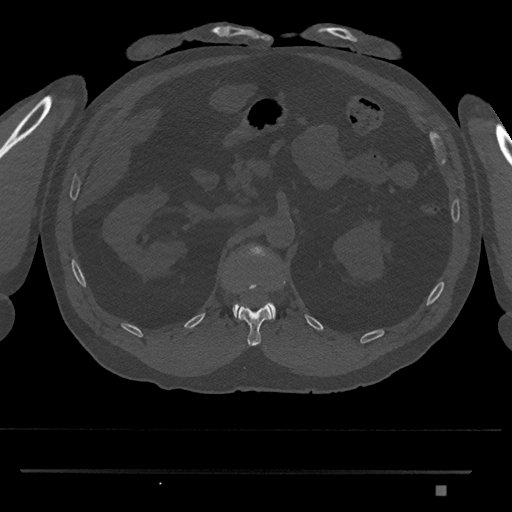
CT including the spine, one axial slice; position 862 of 1134 along the scan axis; bone window (W 1800 / L 400 HU); 0.5 mm slice thickness; 512 × 512 image matrix. Patient: male, 65 years. Case-level facts recorded for this patient, not image findings: primary cancer: prostate.
Structures marked on this image (semi-automatically segmented with operator editing):
- L1 vertebra: box from (x=232, y=244) to (x=276, y=320) px
- T12 vertebra: (x=237, y=305)–(x=272, y=346)